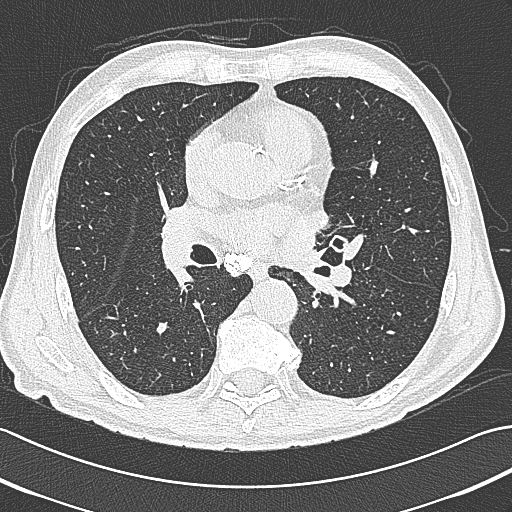
Low-dose screening chest CT, axial slice; first (baseline) screen; lung window (W 1500 / L -600 HU); 120 kVp; slice 185 of 380 in the series. Male, age 65 years at enrolment.
• Lesion marked by an expert reader, bounding box <305,233,358,272> (left, top, right, bottom; pixels).
• Screening reader's record for this exam: no non-calcified nodule ≥4 mm recorded.
• Participant outcome: lung cancer diagnosed 161 days after this screen — large cell neuroendocrine carcinoma, left hilum, left main stem bronchus, stage IIIB (AJCC 6th edition), 70 mm at pathology.